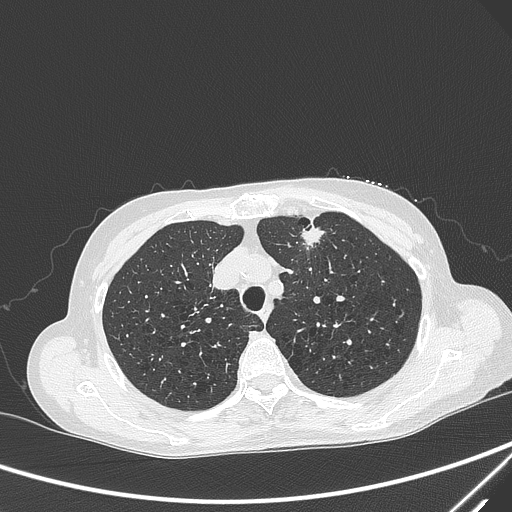
Chest CT, one axial slice. Slice 233 of 299 in the series (ordered by position). Lung window (W 1500 / L -600 HU). 512 × 512 image matrix, field of view 350 × 350 mm. Patient: female, 71 years. Case-level facts recorded for this patient, not image findings: clinical TNM (as recorded): T1c N0 M0.
Structures marked on this image (rectangle marked by the reading radiologist):
- lung tumour (recorded histology: adenocarcinoma): box from (x=298, y=213) to (x=328, y=253) px